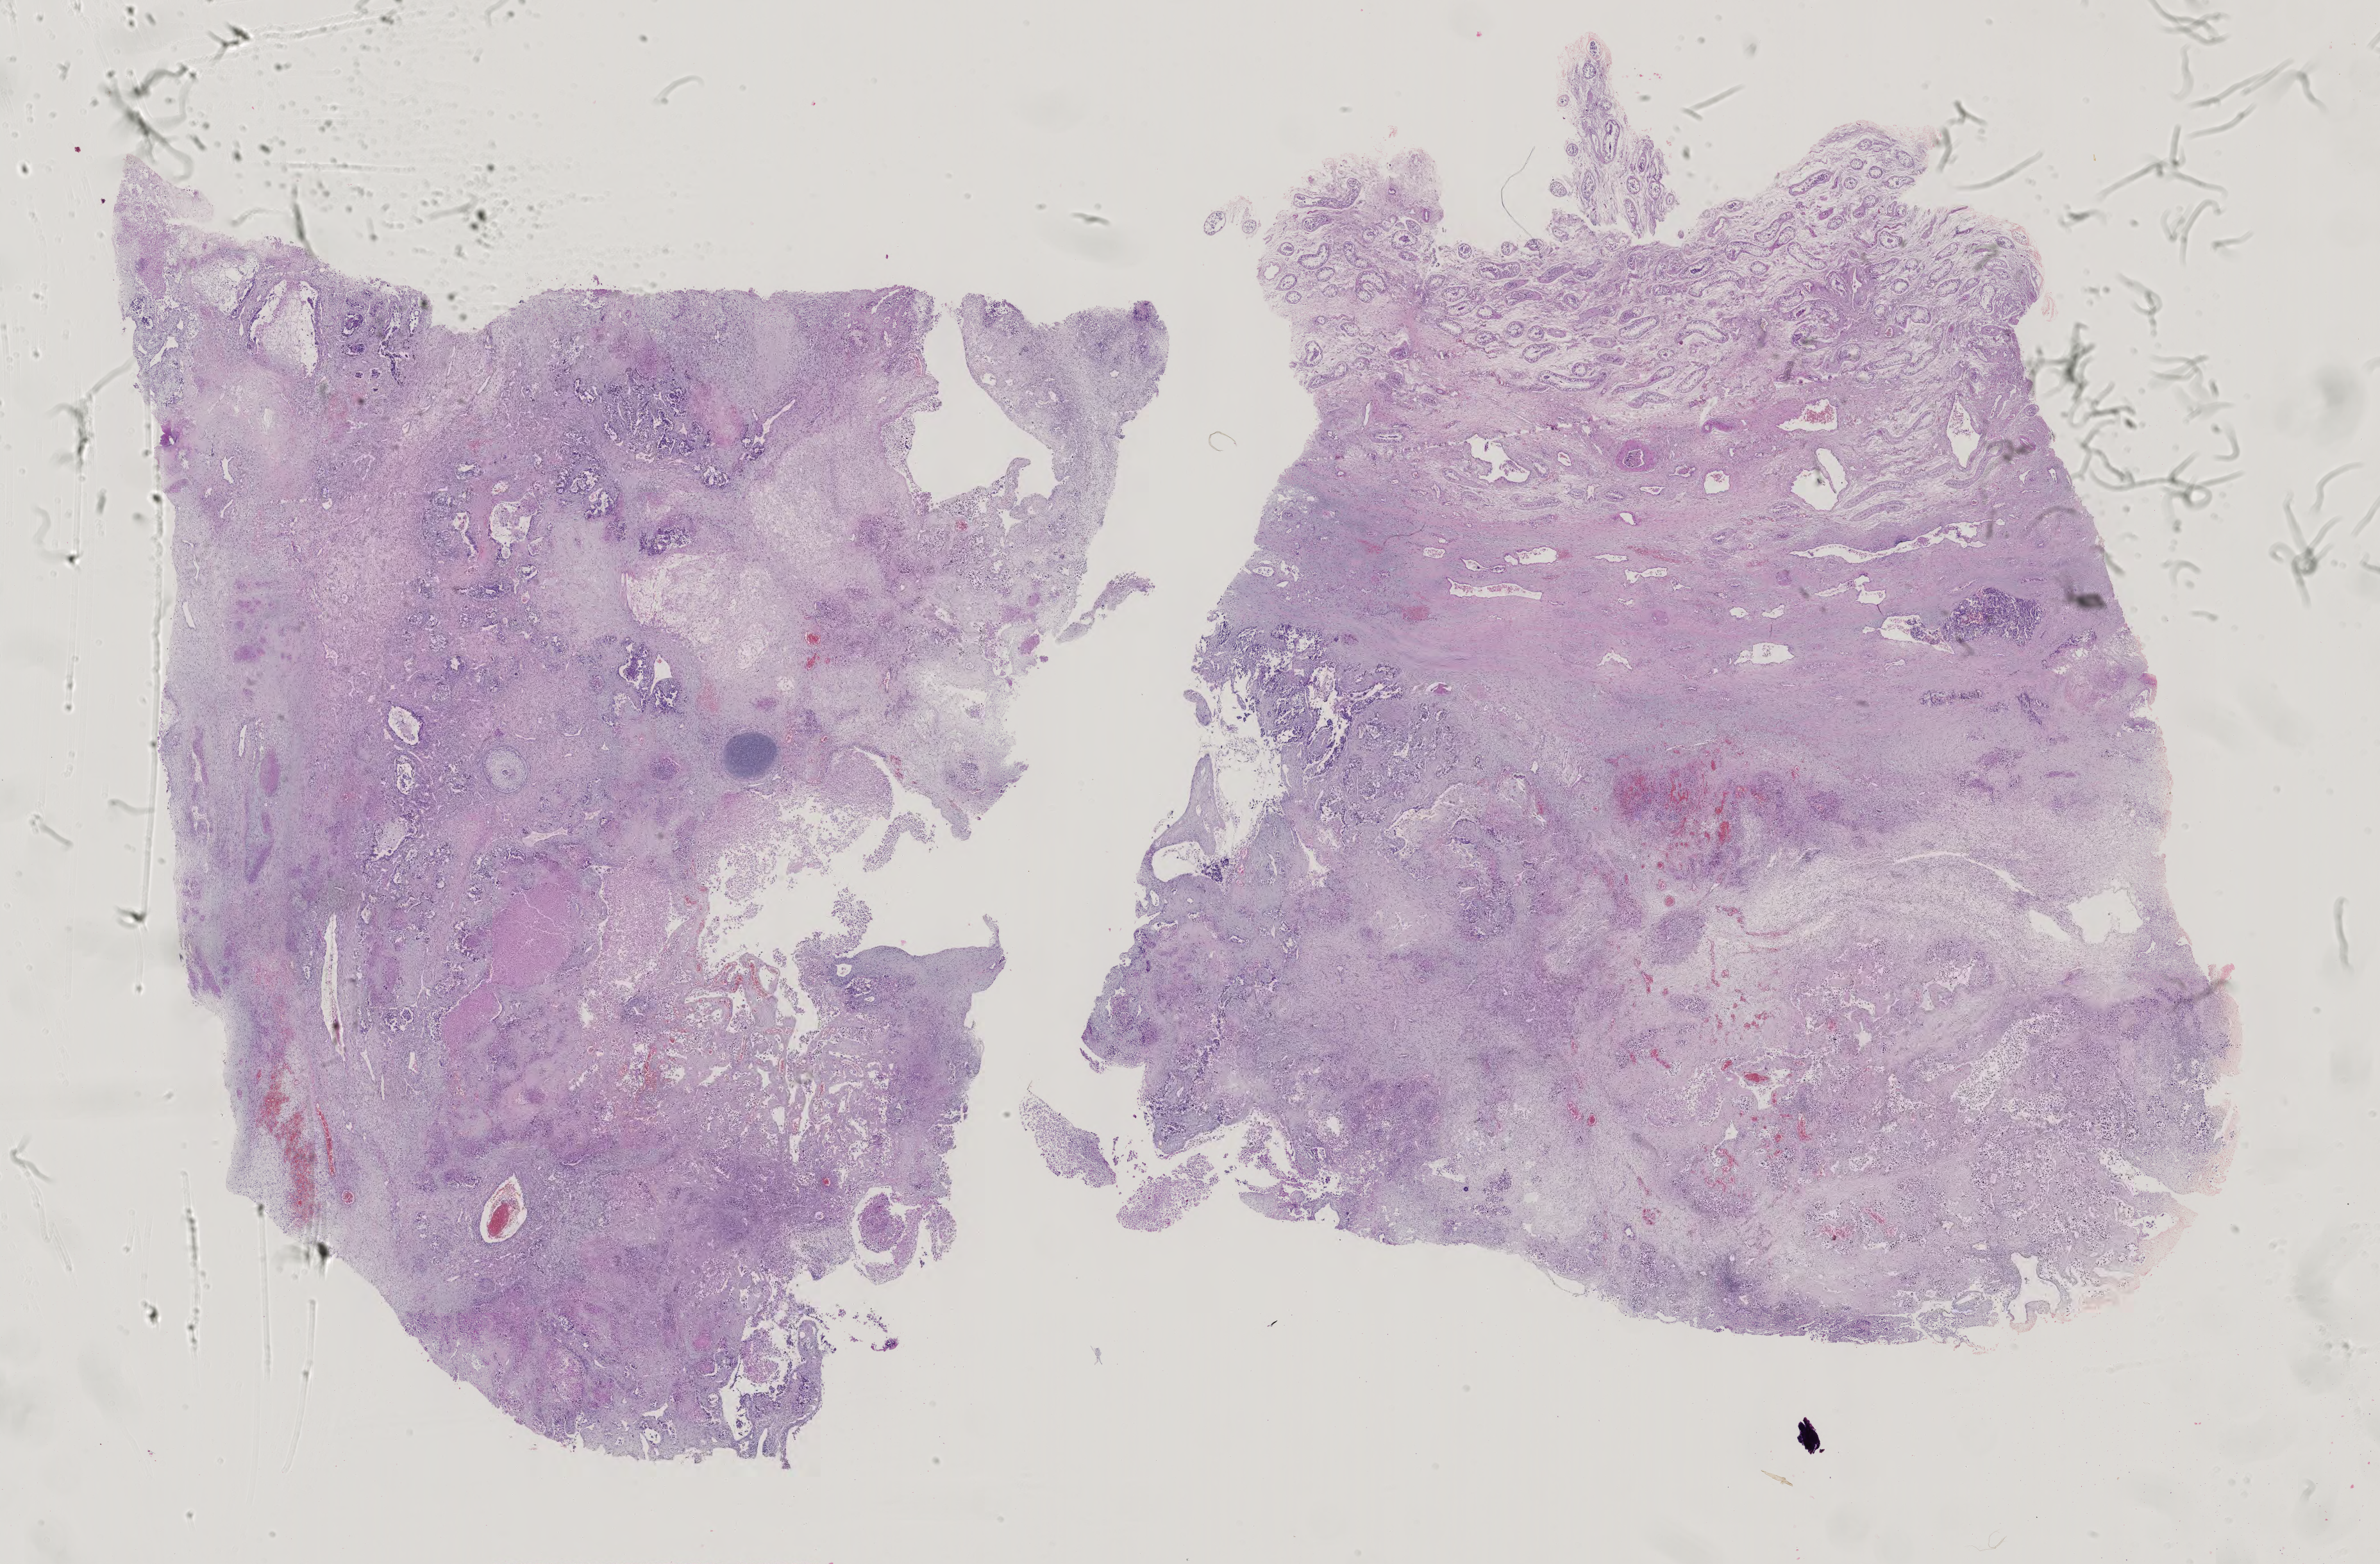
Digitized H&E tissue section (whole slide) — shown as a low-resolution overview of the whole scanned area (about 27.0 x 17.8 mm, from a 40x scan); FFPE section; testis, primary tumour sample. Patient: male, age at initial diagnosis 14 years.
Pathologic diagnosis: Mixed germ cell tumor.